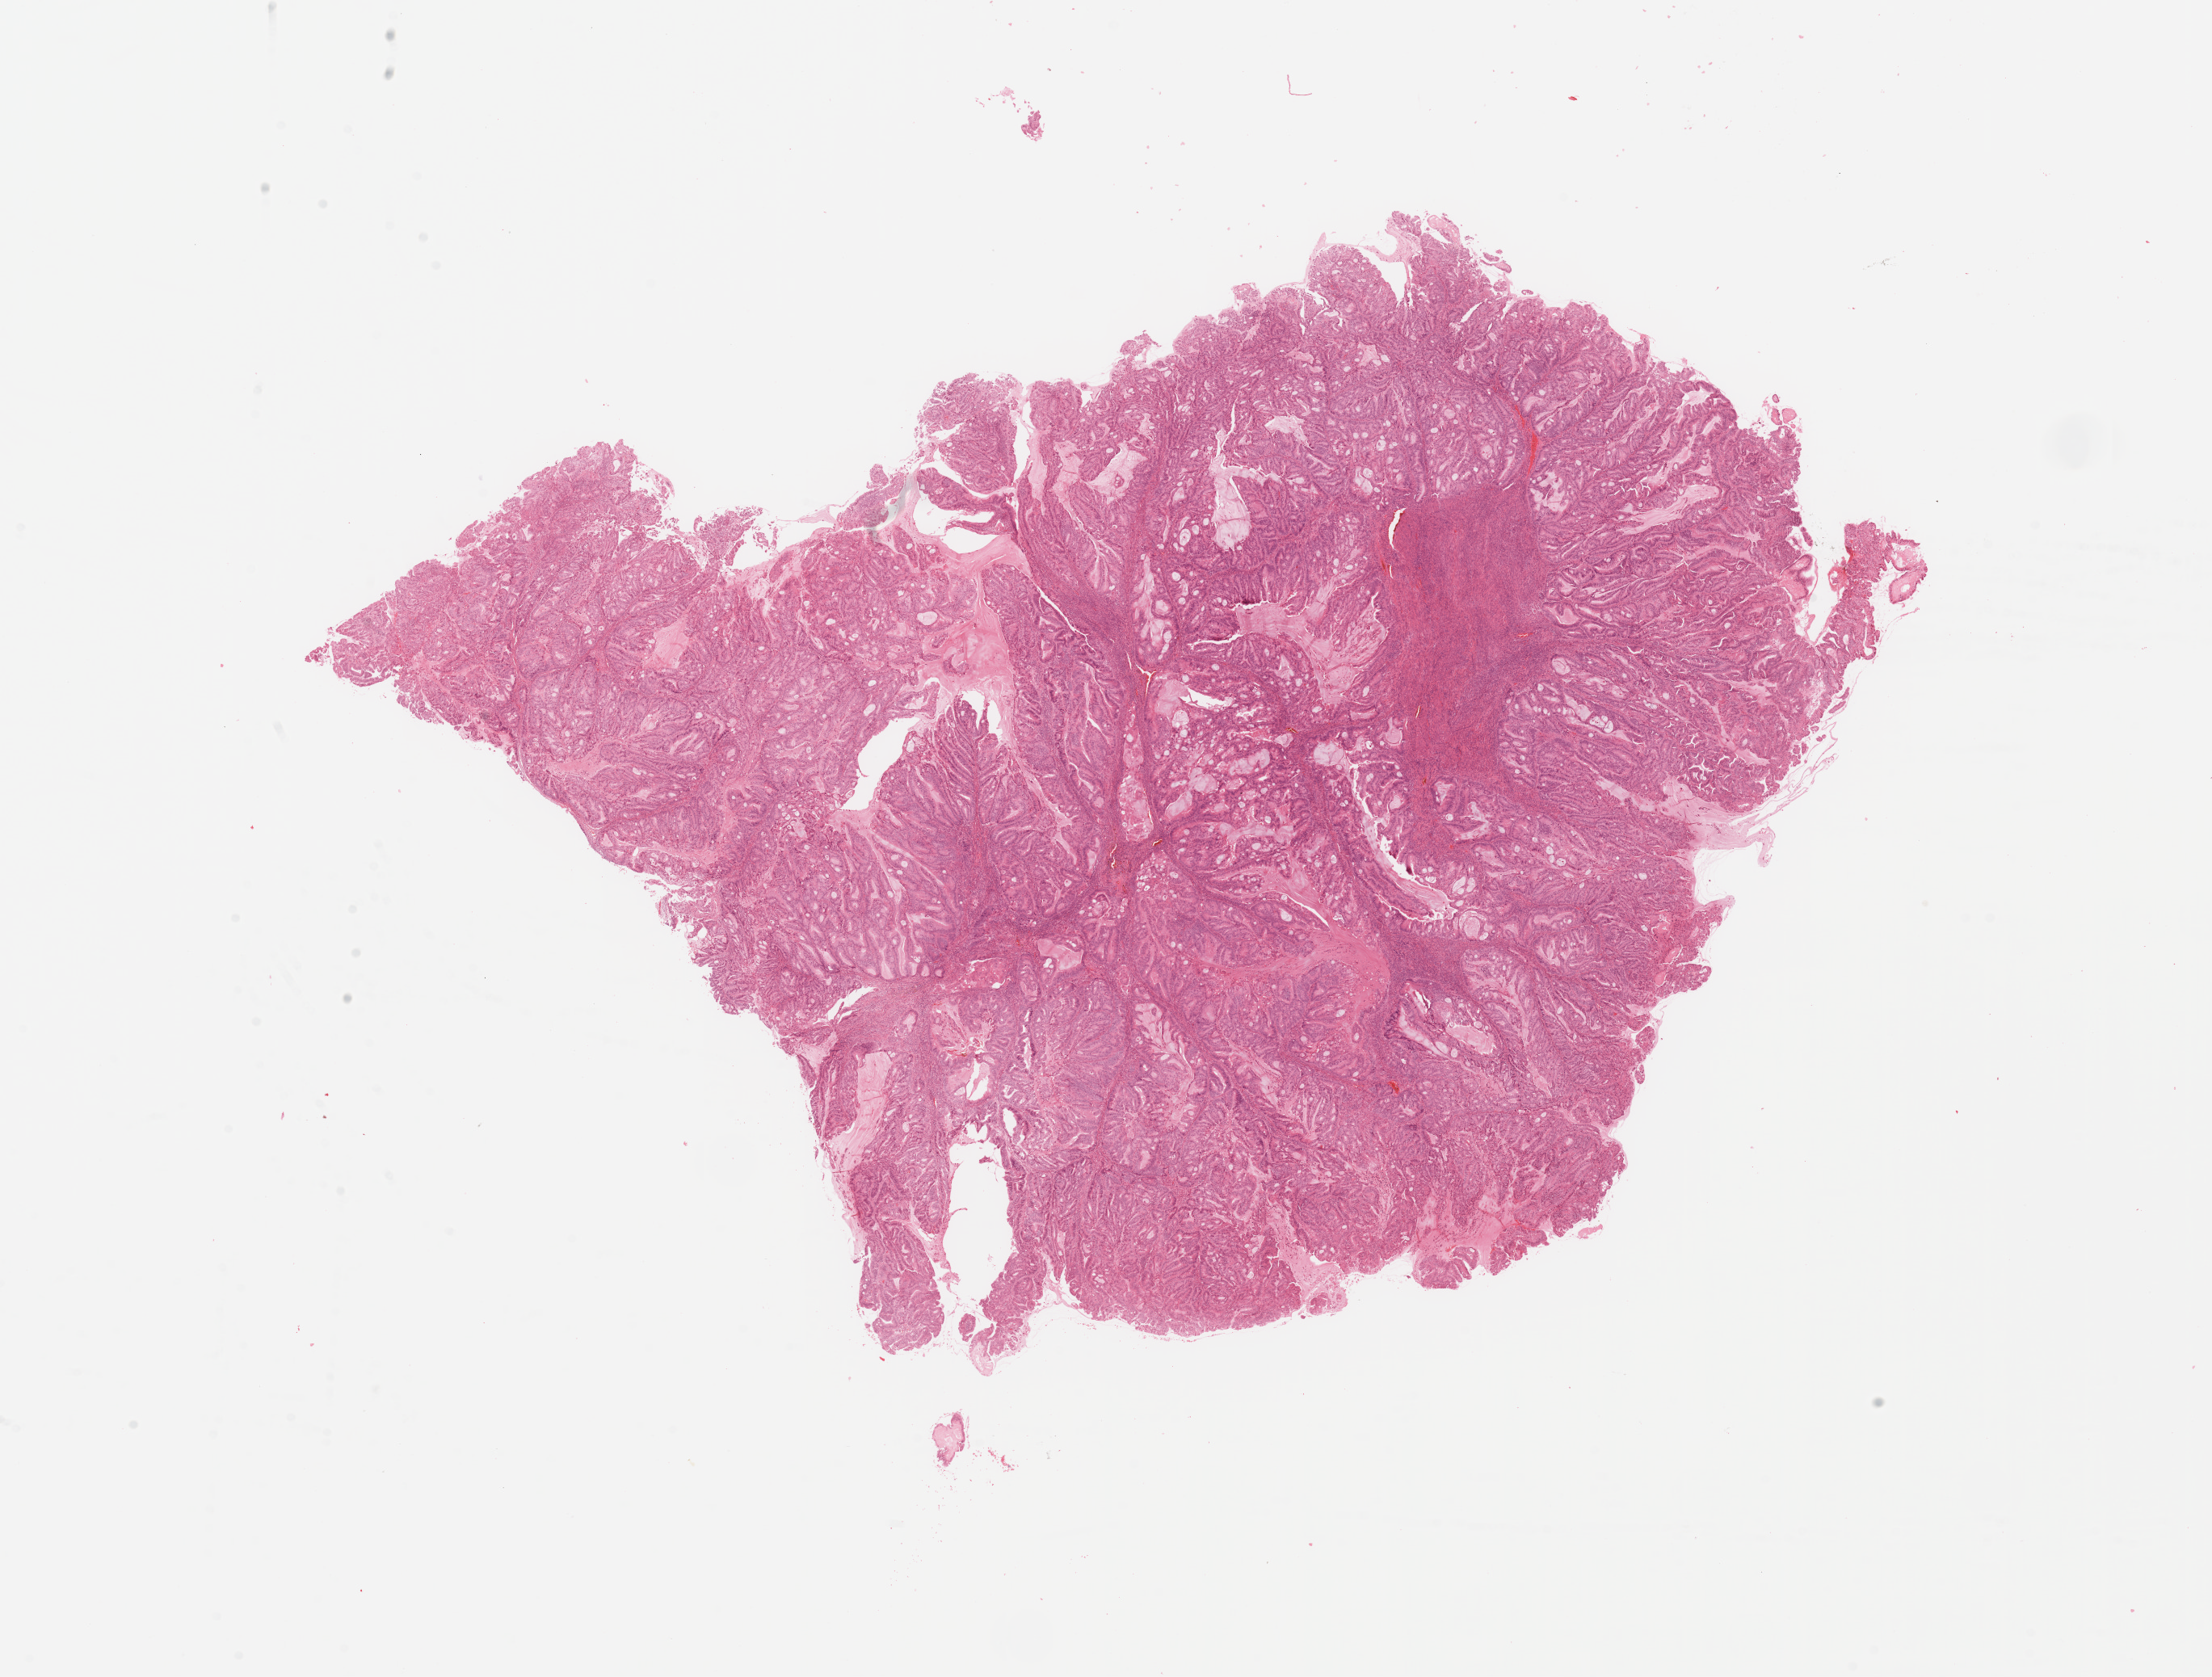
Hematoxylin and eosin (H&E) stained whole-slide image, whole scanned area (about 21.7 x 16.4 mm) shown as a low-resolution overview; tumour tissue sample, sampled site: uterus. Patient: female, age 77 years. Histologic grade: G1 (well differentiated). Slide review estimates, as recorded: tumour nuclei 90%, necrosis 0%.
Diagnosis: Endometrioid adenocarcinoma, NOS.